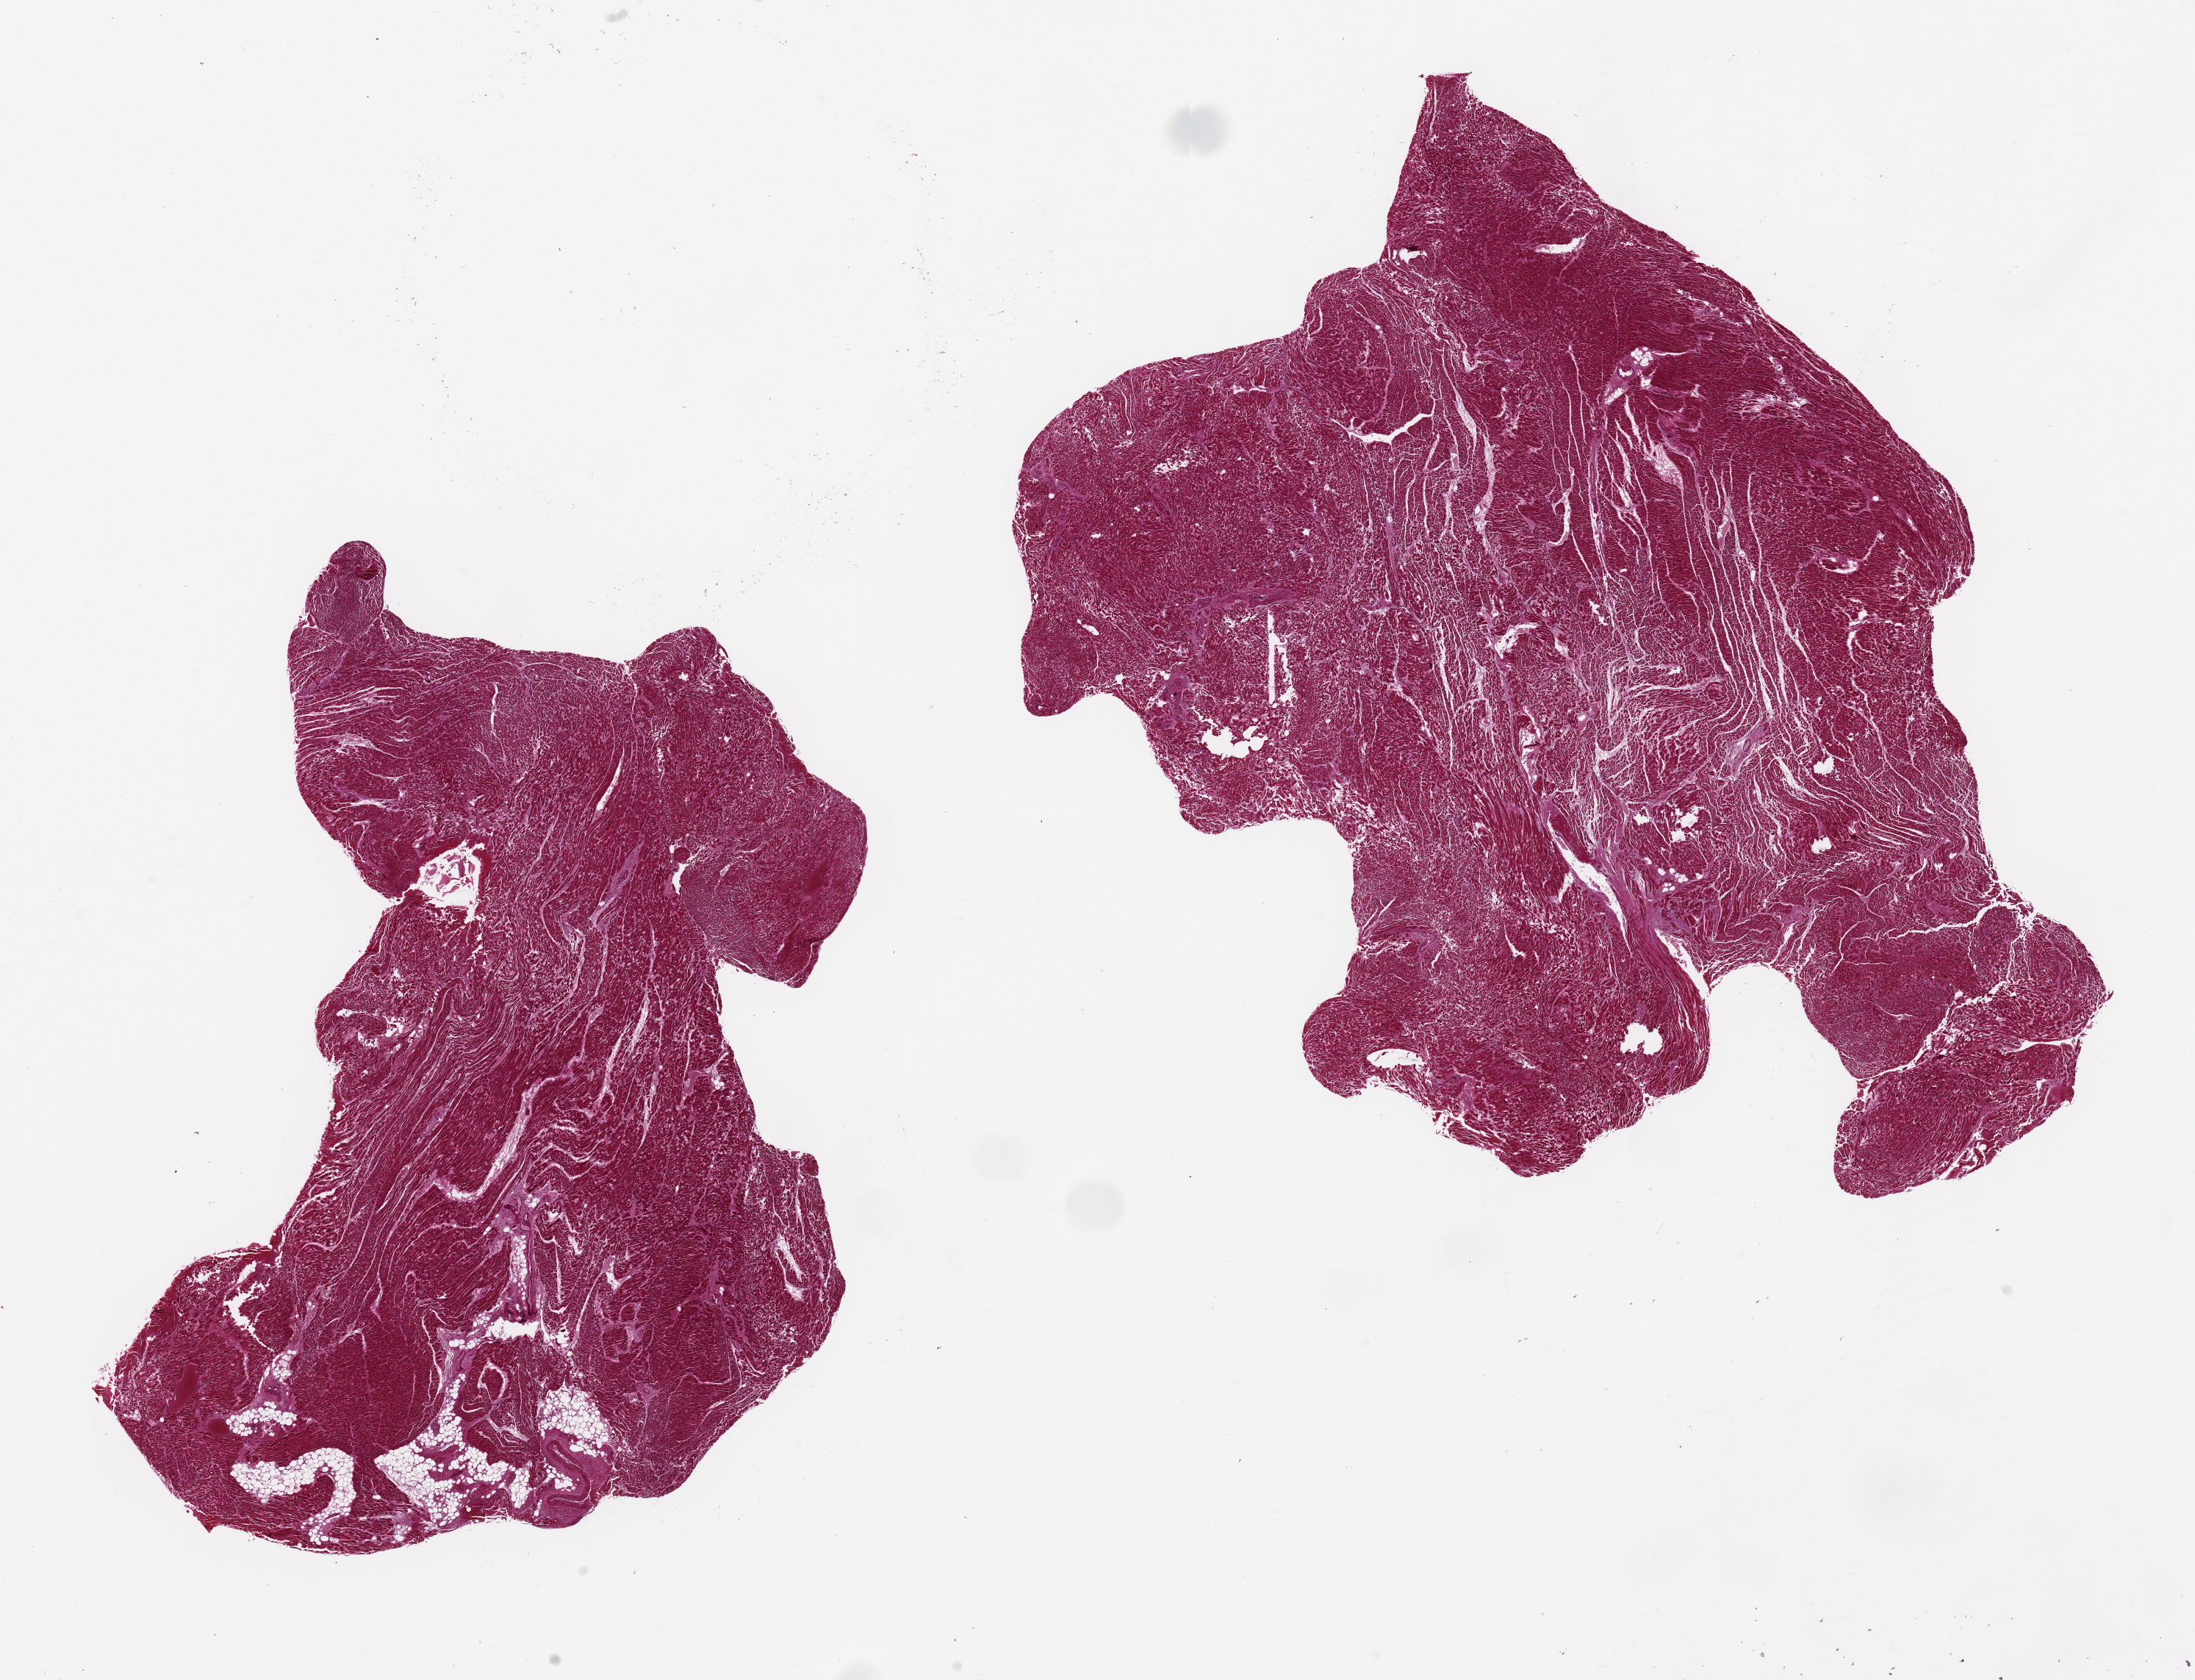
Whole-slide image, hematoxylin and eosin (H&E) stain, low-resolution overview of the scanned area, about 23.6 x 18.1 mm (slide scanned at 20x). PAXgene-fixed paraffin-embedded (PFPE) section. Target tissue: heart. Tissue donor sample. Donor sex: female.
* reviewer comment on this tissue sample: 2 aliquots, ~11x8mm